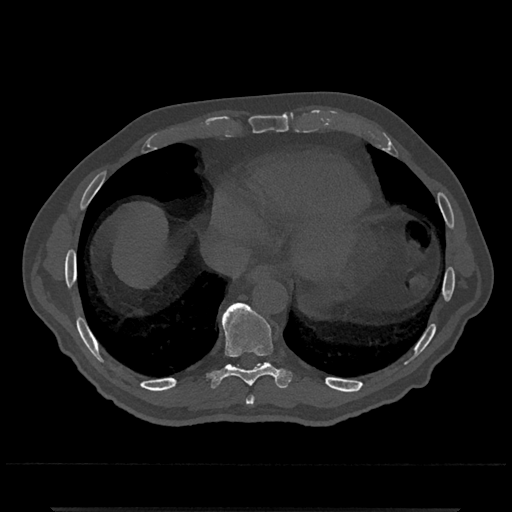
CT including the spine, one axial slice; slice 609 of 797 in the series (ordered by position); reconstruction kernel Br40s/3; bone window (W 1800 / L 400 HU); 0.5 mm slice thickness; 512 × 512 image matrix. Male patient, age 67 years. Case-level facts recorded for this patient, not image findings: primary cancer: prostate.
Outlined on this slice (semi-automatically segmented with operator editing):
- T8 vertebra: box from (x=246, y=396) to (x=255, y=405) px
- T9 vertebra: (x=207, y=302)–(x=292, y=388)